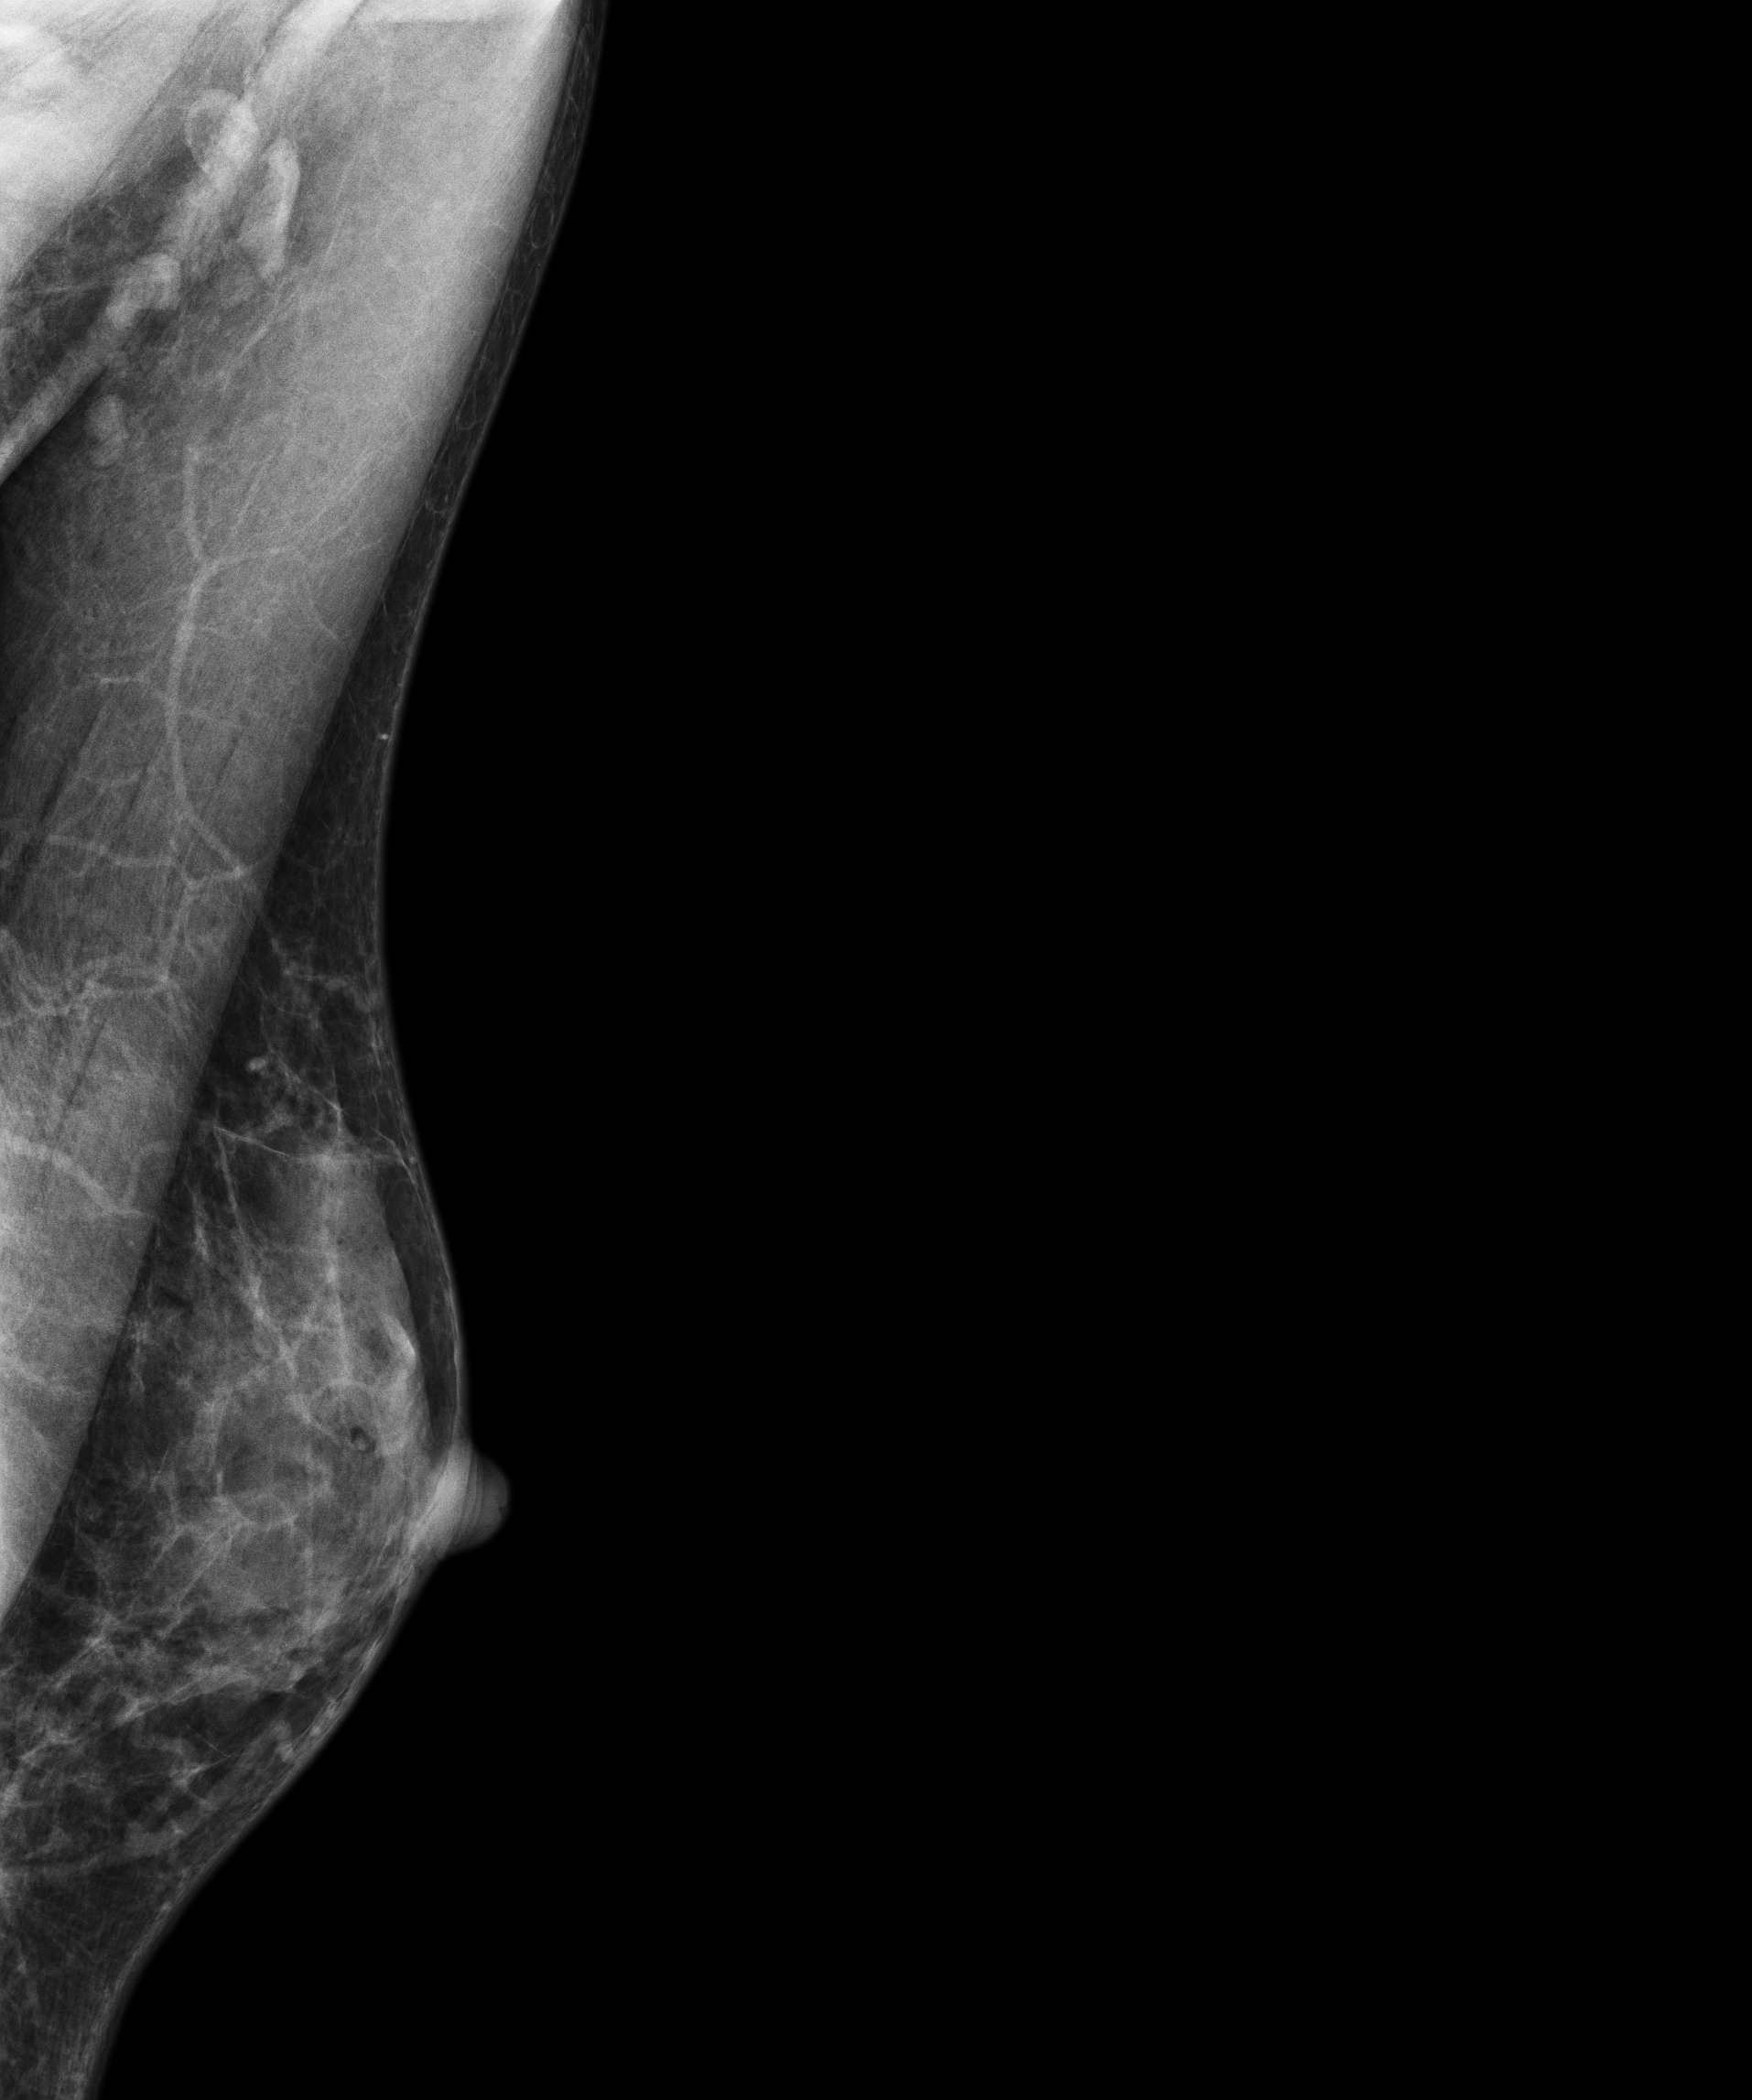
Screening examination; compressed breast thickness 34 mm. Patient aged 56 years (female).
Image type: full-field digital mammogram. Breast: left. Projection: MLO view.